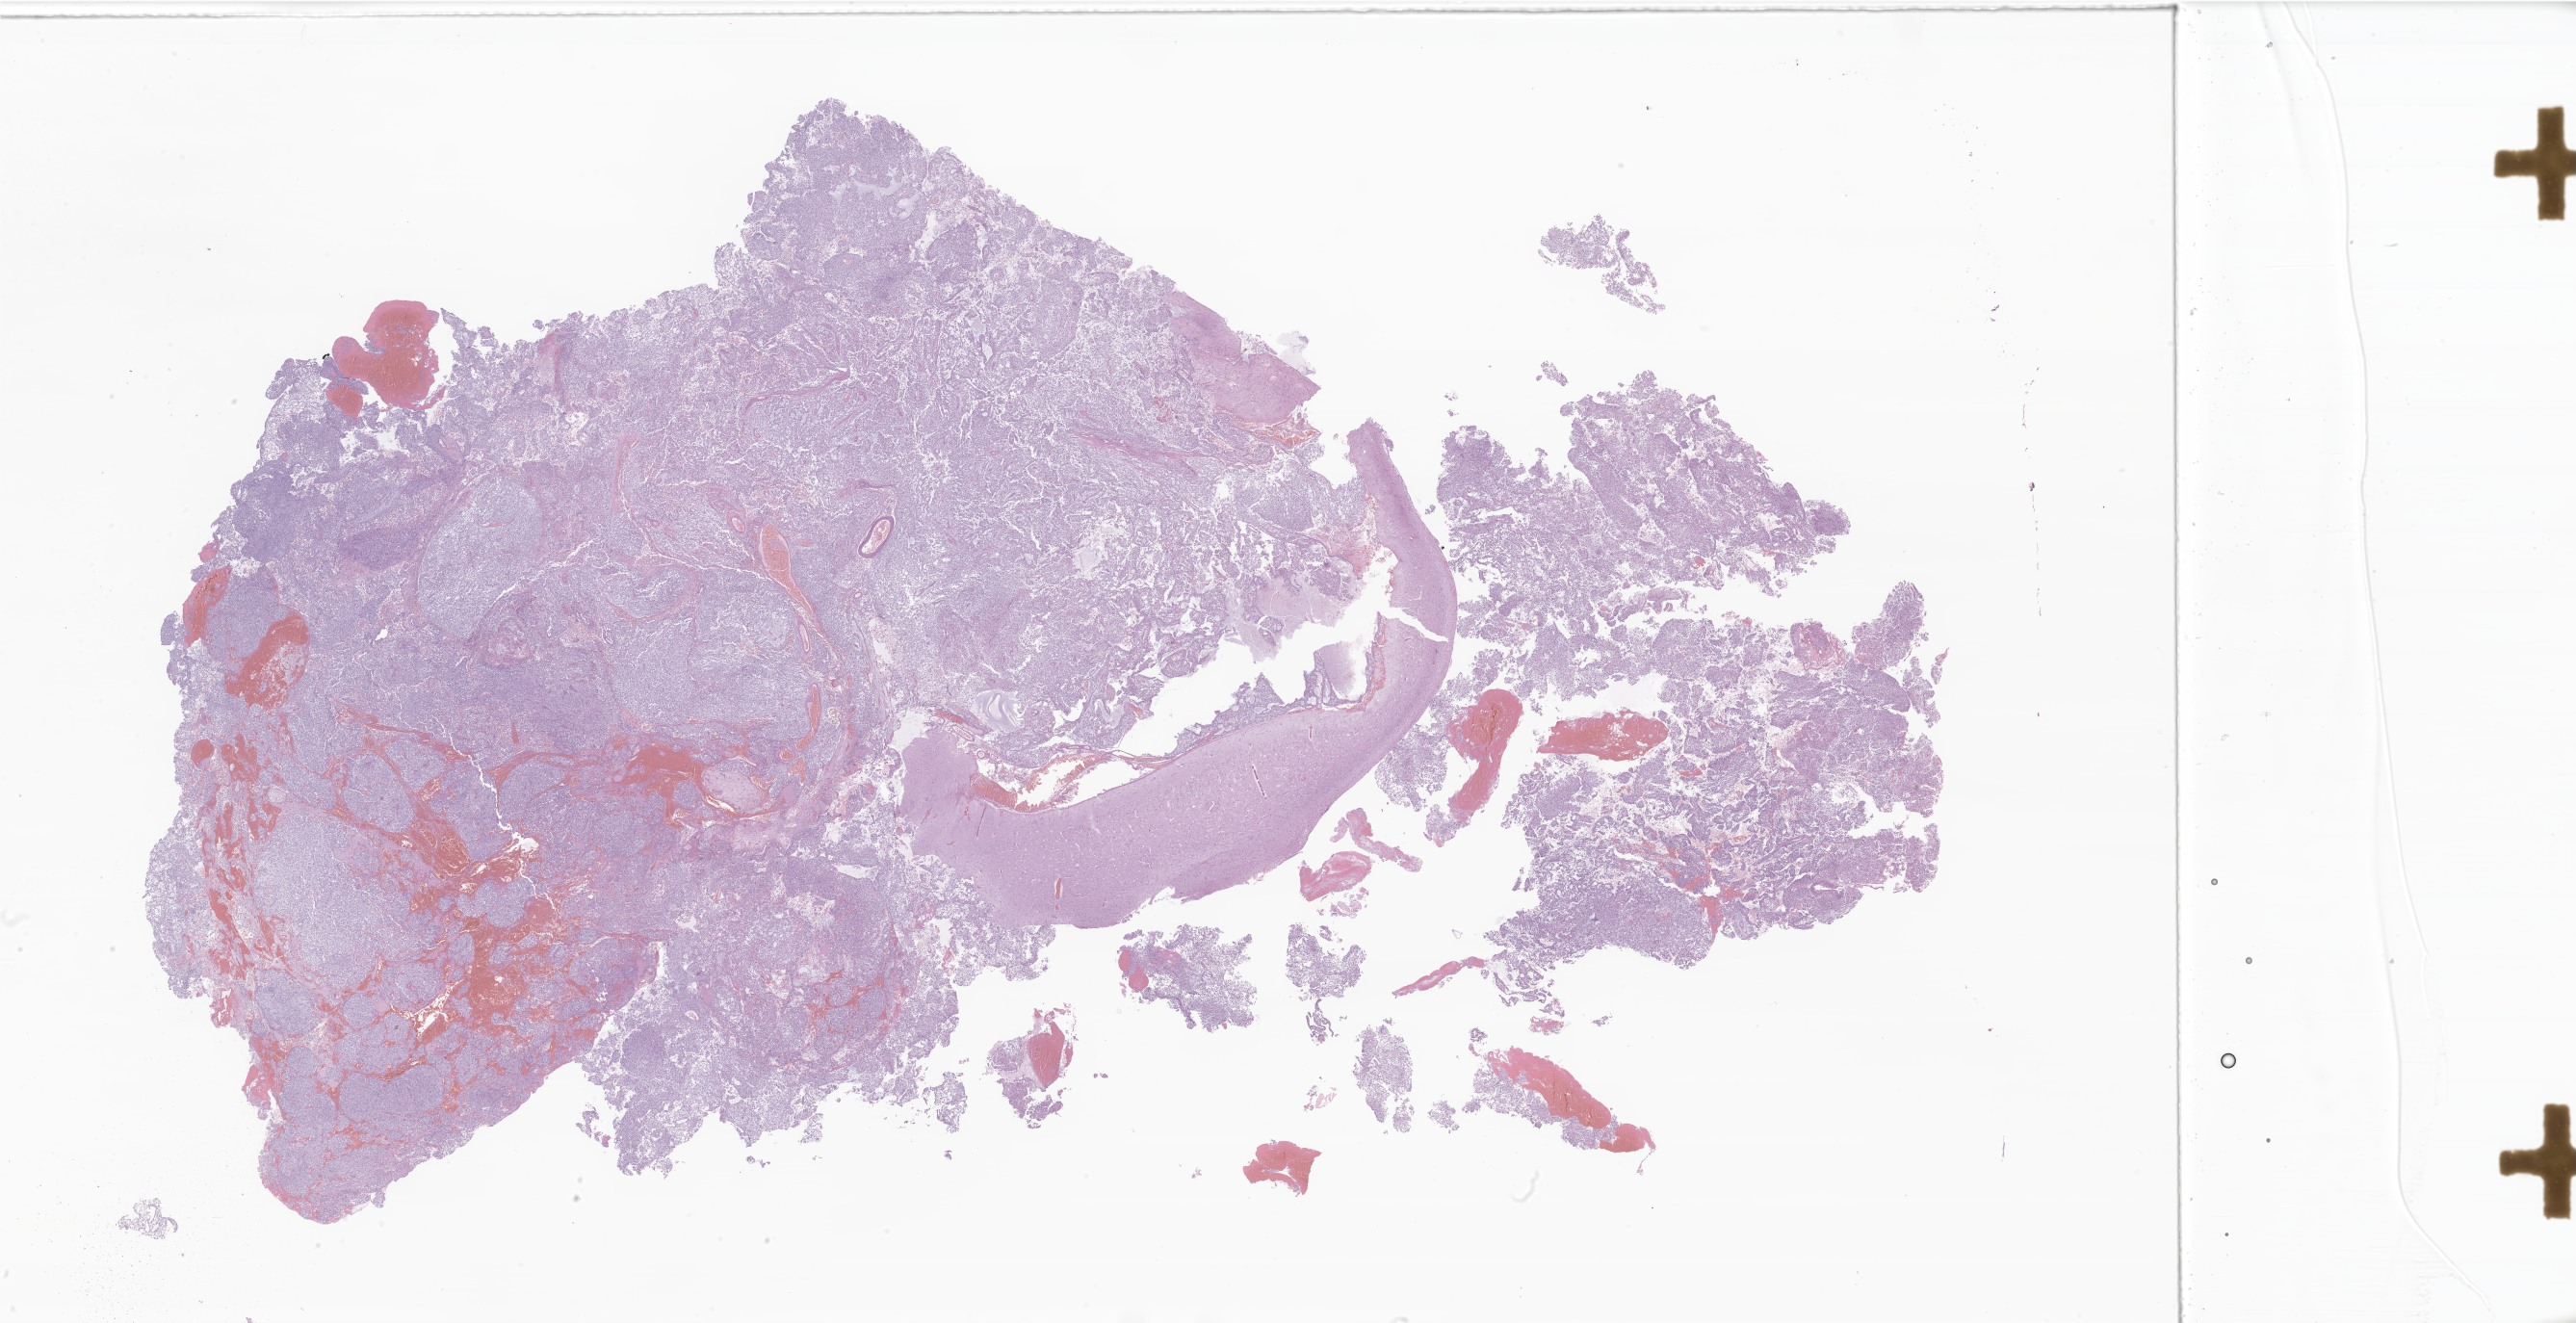
H&E whole-slide image of tumor tissue from the brain — a low-resolution overview of the entire scanned area, about 45.1 x 23.2 mm, formalin-fixed paraffin-embedded section. Patient: female, age 80 months (6 years 8 months).
• diagnosis (ICD-O-3 morphology term): Ependymoma, NOS